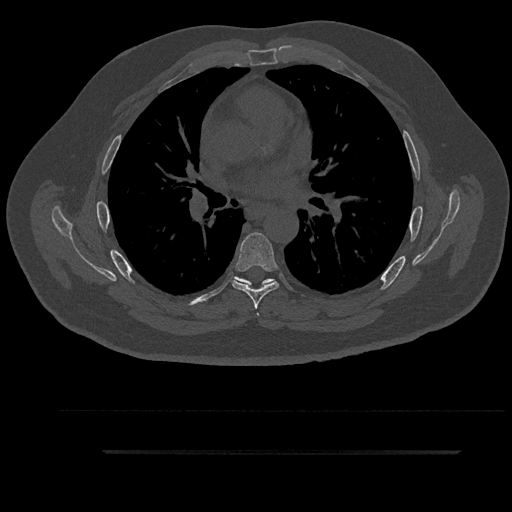
CT including the spine, one axial slice. Position 570 of 797 along the scan axis. 120 kVp. Bone window (W 1800 / L 400 HU). 0.5 mm slice thickness. 512 × 512 image matrix. Male patient, age 63 years. From the clinical record (not read from this slice): primary cancer: renal.
Annotated regions visible in this slice (semi-automatically segmented with operator editing):
- T5 vertebra: bounding box <235,277,274,316> (left, top, right, bottom; pixels)
- T6 vertebra: <232,232,279,309>
- T7 vertebra: <240,278,275,286>